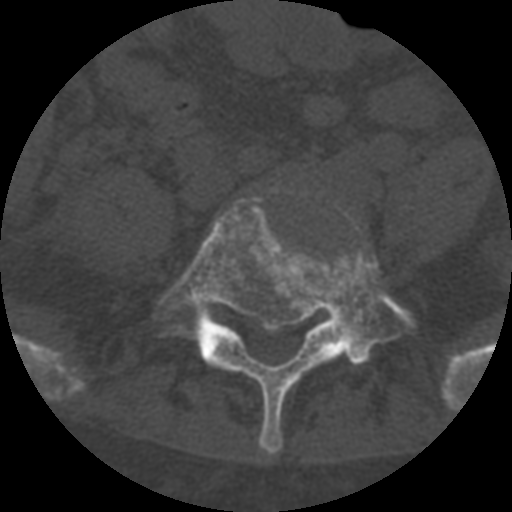
CT including the spine, one axial slice; slice 186 of 708 in the series (ordered by position); 120 kVp; one of 3 acquisitions stored at this slice position; bone window (W 1800 / L 400 HU); 512 × 512 image matrix. Patient age 55 years. From the clinical record (not read from this slice): primary cancer: colon.
Annotated regions visible in this slice (semi-automatic segmentation, software-assisted and operator-edited):
- L5 vertebra: bounding box <151,187,417,455> (left, top, right, bottom; pixels)